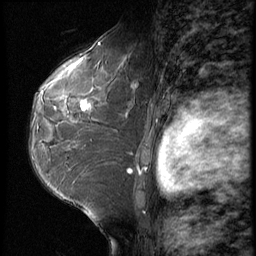
Breast MRI (dynamic contrast-enhanced), one sagittal slice; slice 42 of 62 in the series (ordered by position); 3 images stored at this slice position (order not interpretable as contrast timing); 1.5 T; TE 4.2 ms, TR 9 ms; 2.5 mm slice thickness; 256 × 256 image matrix, field of view 180 × 180 mm. Female patient, age 50 years. From the clinical record (not read from this slice): setting: breast cancer imaged before/during neoadjuvant chemotherapy; receptor status: HR-positive, HER2-negative.
Annotated regions visible in this slice (semi-automatic segmentation, software-assisted and operator-edited):
- analysis volume of interest (the breast-tissue region the enhancement analysis was run in; not a lesion): bounding box (x1, y1, x2, y2) in pixels: (32, 91, 118, 209)
- tumour enhancement mask (voxels above the 140 % enhancement threshold inside the analysis volume of interest): (82, 104, 91, 108)